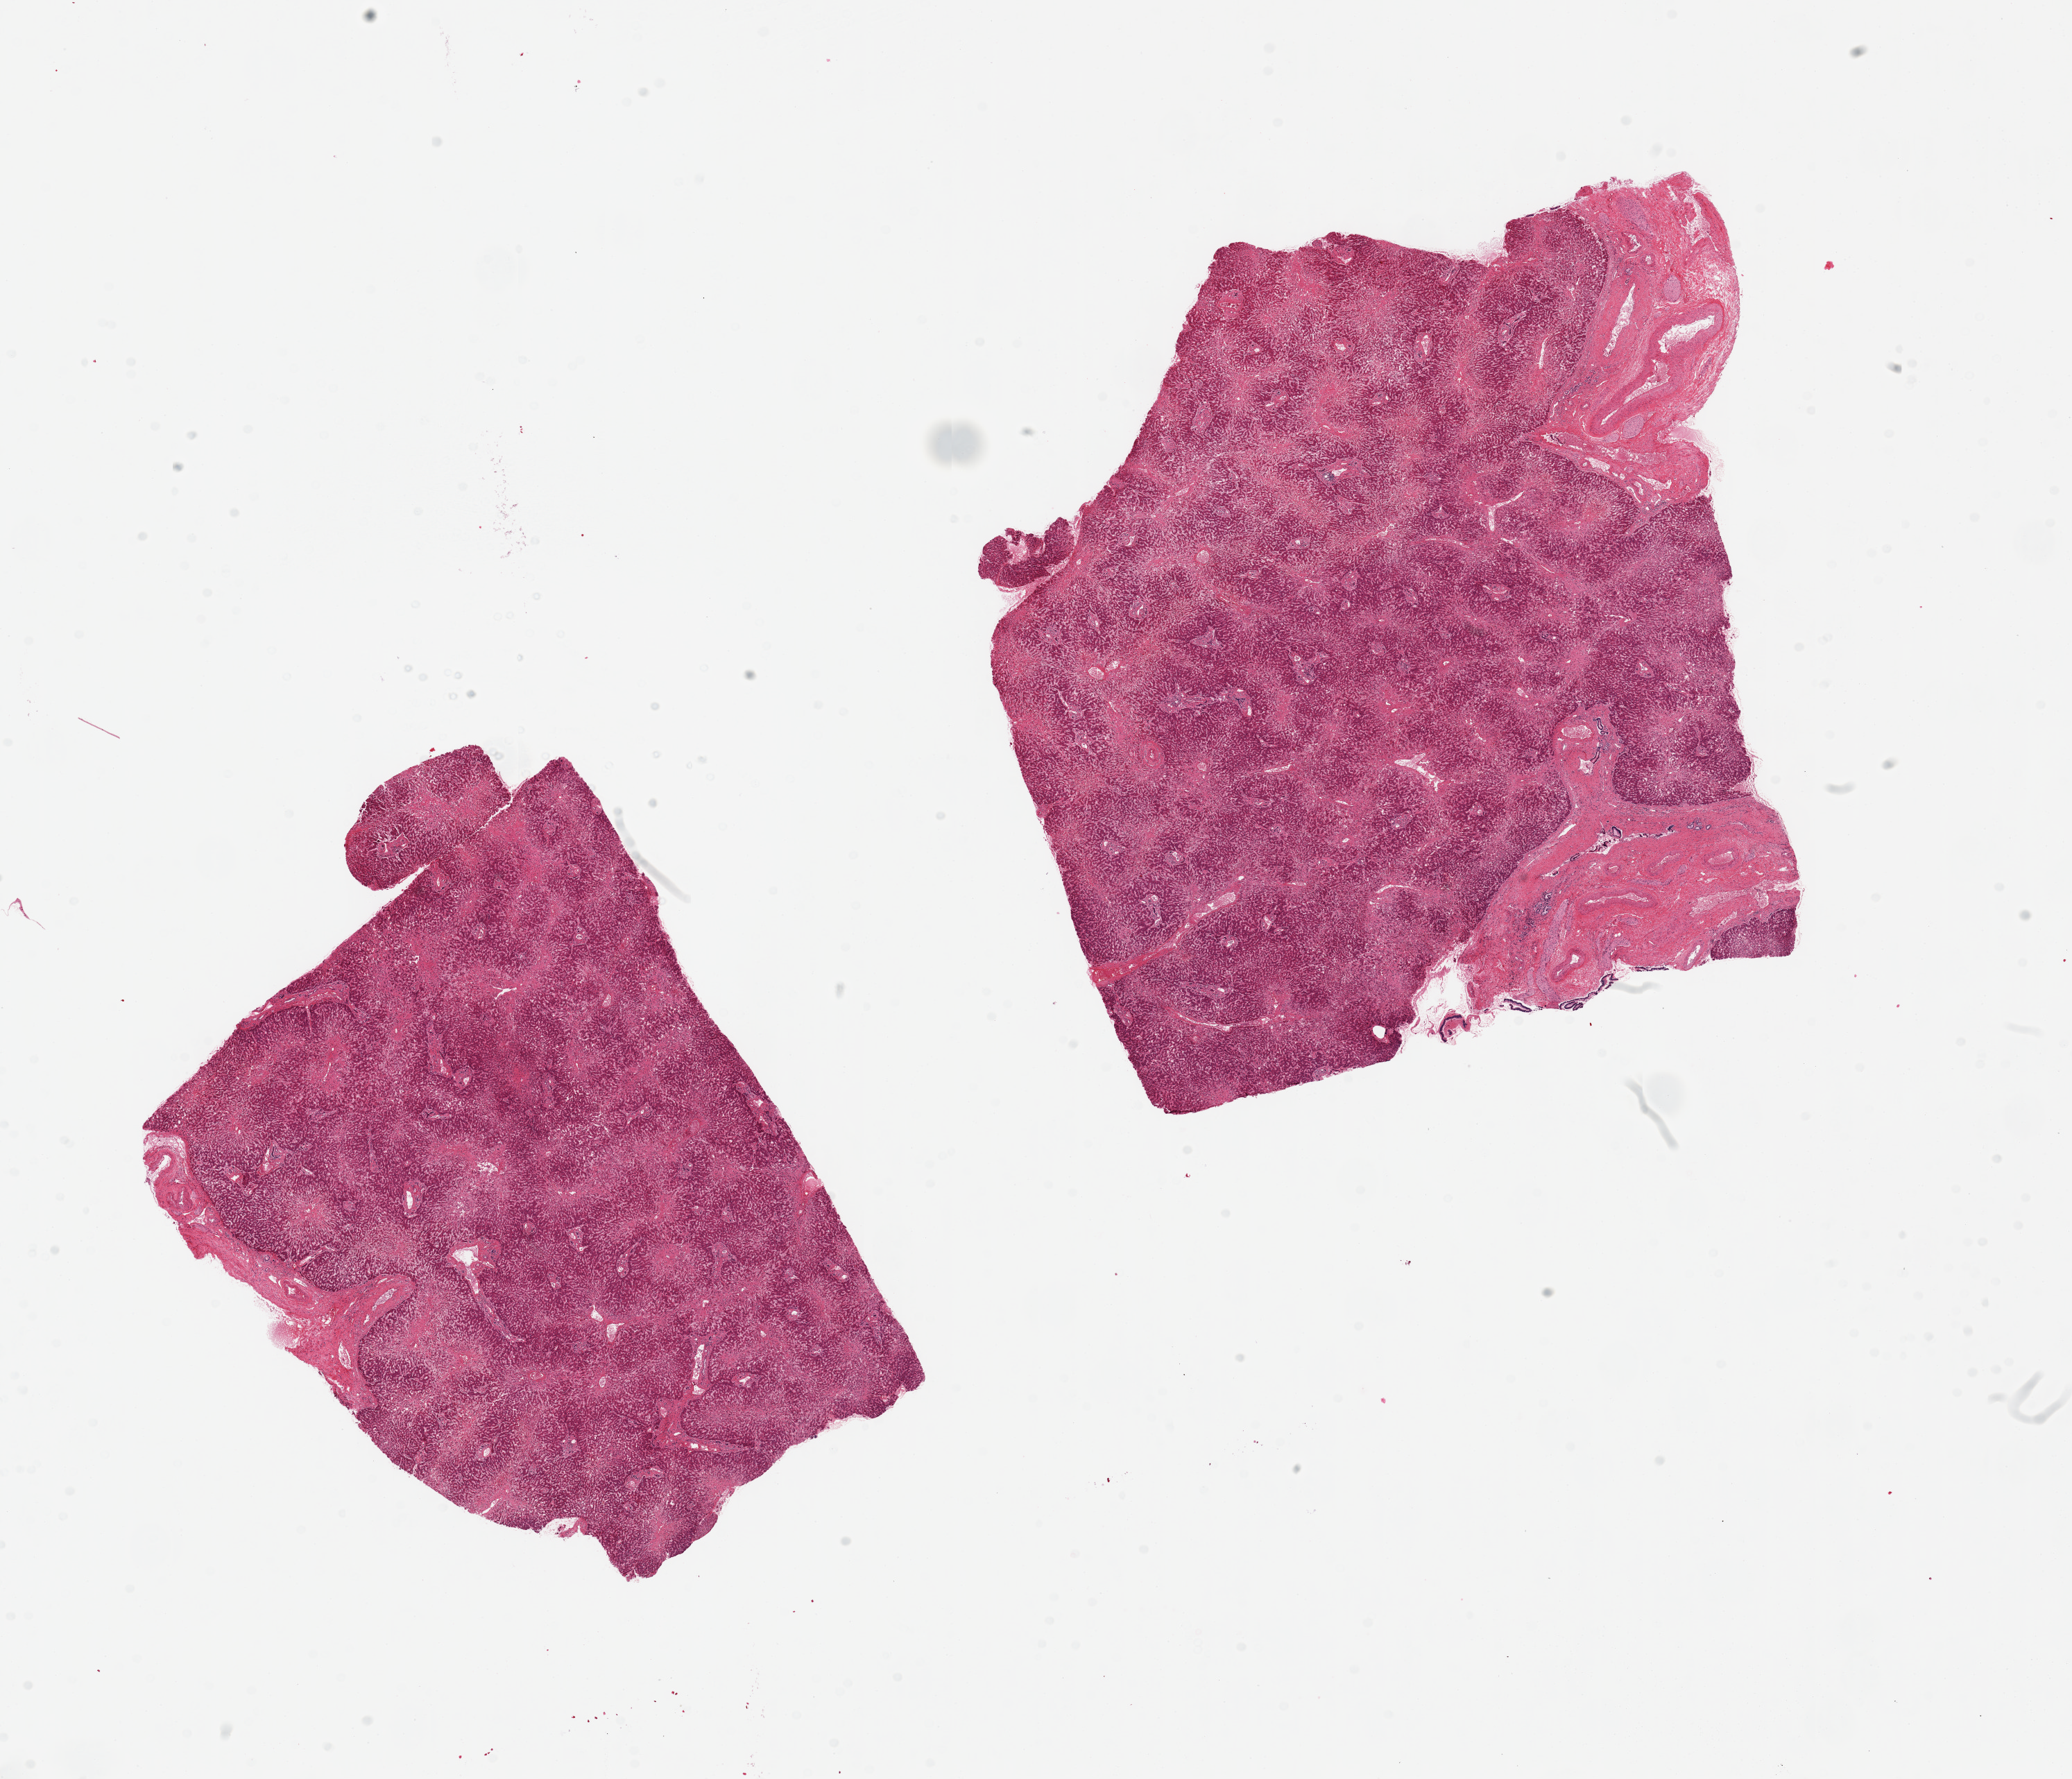
H&E whole-slide image, brightfield, low-resolution overview of the scanned area, about 23.6 x 20.3 mm, PAXgene-fixed paraffin-embedded (PFPE) section, section of liver (target tissue), tissue donor sample. Donor: male.
Review note (as recorded): 2 pieces, 9x6.5 & 10x8mm; cardiac cirrhosis:central atrophy and fibrosis with early bridging; large vessels on 2 edges of 1 piece (~20% of piece).